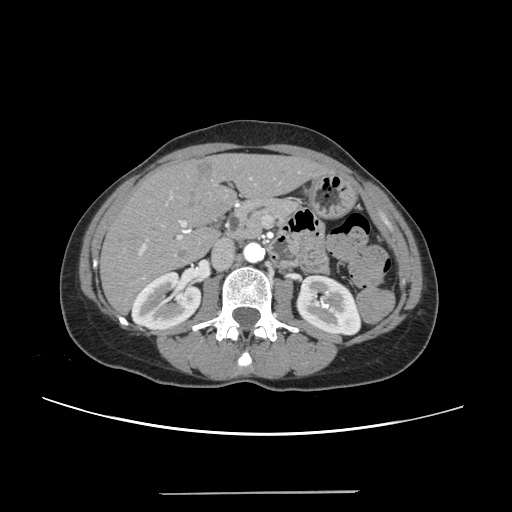
Contrast-enhanced abdominal CT, one axial slice. Position 115 of 240 along the scan axis. 120 kVp. Soft-tissue window (W 400 / L 40 HU). 1.25 mm slice thickness. 512 × 512 image matrix. Female patient, age 60 years. From the clinical record (not read from this slice): diagnosis: colorectal cancer liver metastases, imaged before liver resection; multiple liver metastases: no; largest metastasis: 1.5 cm; disease in both lobes: no.
Outlined on this slice (expert manual segmentation):
- liver: bounding box (x1, y1, x2, y2) in pixels: (102, 154, 327, 312)
- planned liver remnant (the part of the liver to remain after resection): (102, 155, 327, 311)
- portal vein (with intrahepatic branches): (138, 177, 252, 278)
- liver metastasis: (196, 163, 214, 178)